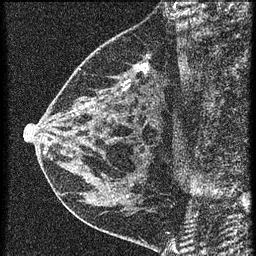
Breast MRI (dynamic contrast-enhanced), one sagittal slice; position 24 of 60 along the scan axis; 3 images stored at this slice position (order not interpretable as contrast timing); 1.5 T; TE 4.2 ms, TR 20.4 ms; 256 × 256 image matrix, field of view 180 × 180 mm. Patient: female, 46 years. Case-level facts recorded for this patient, not image findings: setting: breast cancer imaged before/during neoadjuvant chemotherapy; receptor status: HR-positive, HER2-negative.
Structures marked on this image (semi-automatically segmented with operator editing):
- analysis volume of interest (the breast-tissue region the enhancement analysis was run in; not a lesion): bounding box <58,36,169,155> (left, top, right, bottom; pixels)
- tumour enhancement mask (voxels above the 90 % enhancement threshold inside the analysis volume of interest): <136,64,147,71>